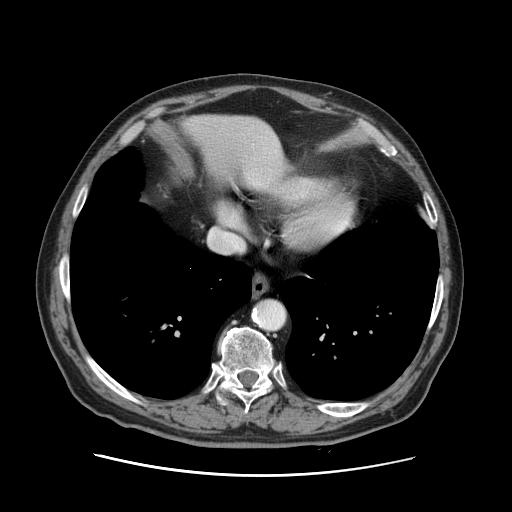
Contrast-enhanced abdominal CT, one axial slice; slice 121 of 141 in the series (ordered by position); 120 kVp; soft-tissue window (W 400 / L 40 HU); 2.5 mm slice thickness; 512 × 512 image matrix. Male patient, age 72 years. Case-level facts recorded for this patient, not image findings: diagnosis: colorectal cancer liver metastases, imaged before liver resection; multiple liver metastases: yes; largest metastasis: 5.4 cm.
Outlined on this slice (outlined manually by an expert reader):
- liver: bounding box (x1, y1, x2, y2) in pixels: (185, 116, 284, 190)
- planned liver remnant (the part of the liver to remain after resection): (186, 116, 283, 190)